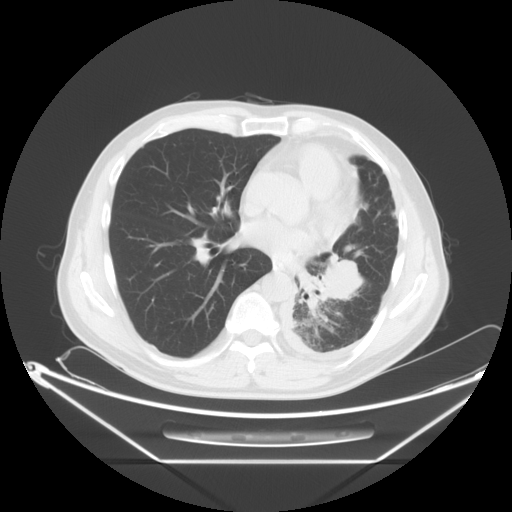
Chest CT, one axial slice. Position 30 of 63 along the scan axis. Reconstruction kernel STANDARD. Lung window (W 1500 / L -600 HU). 512 × 512 image matrix. Patient: male, 60 years. Case-level facts recorded for this patient, not image findings: clinical TNM (as recorded): T4 N1 M1.
Structures marked on this image (rectangle marked by the reading radiologist):
- lung tumour (recorded histology: adenocarcinoma): bounding box (x1, y1, x2, y2) in pixels: (309, 239, 368, 318)